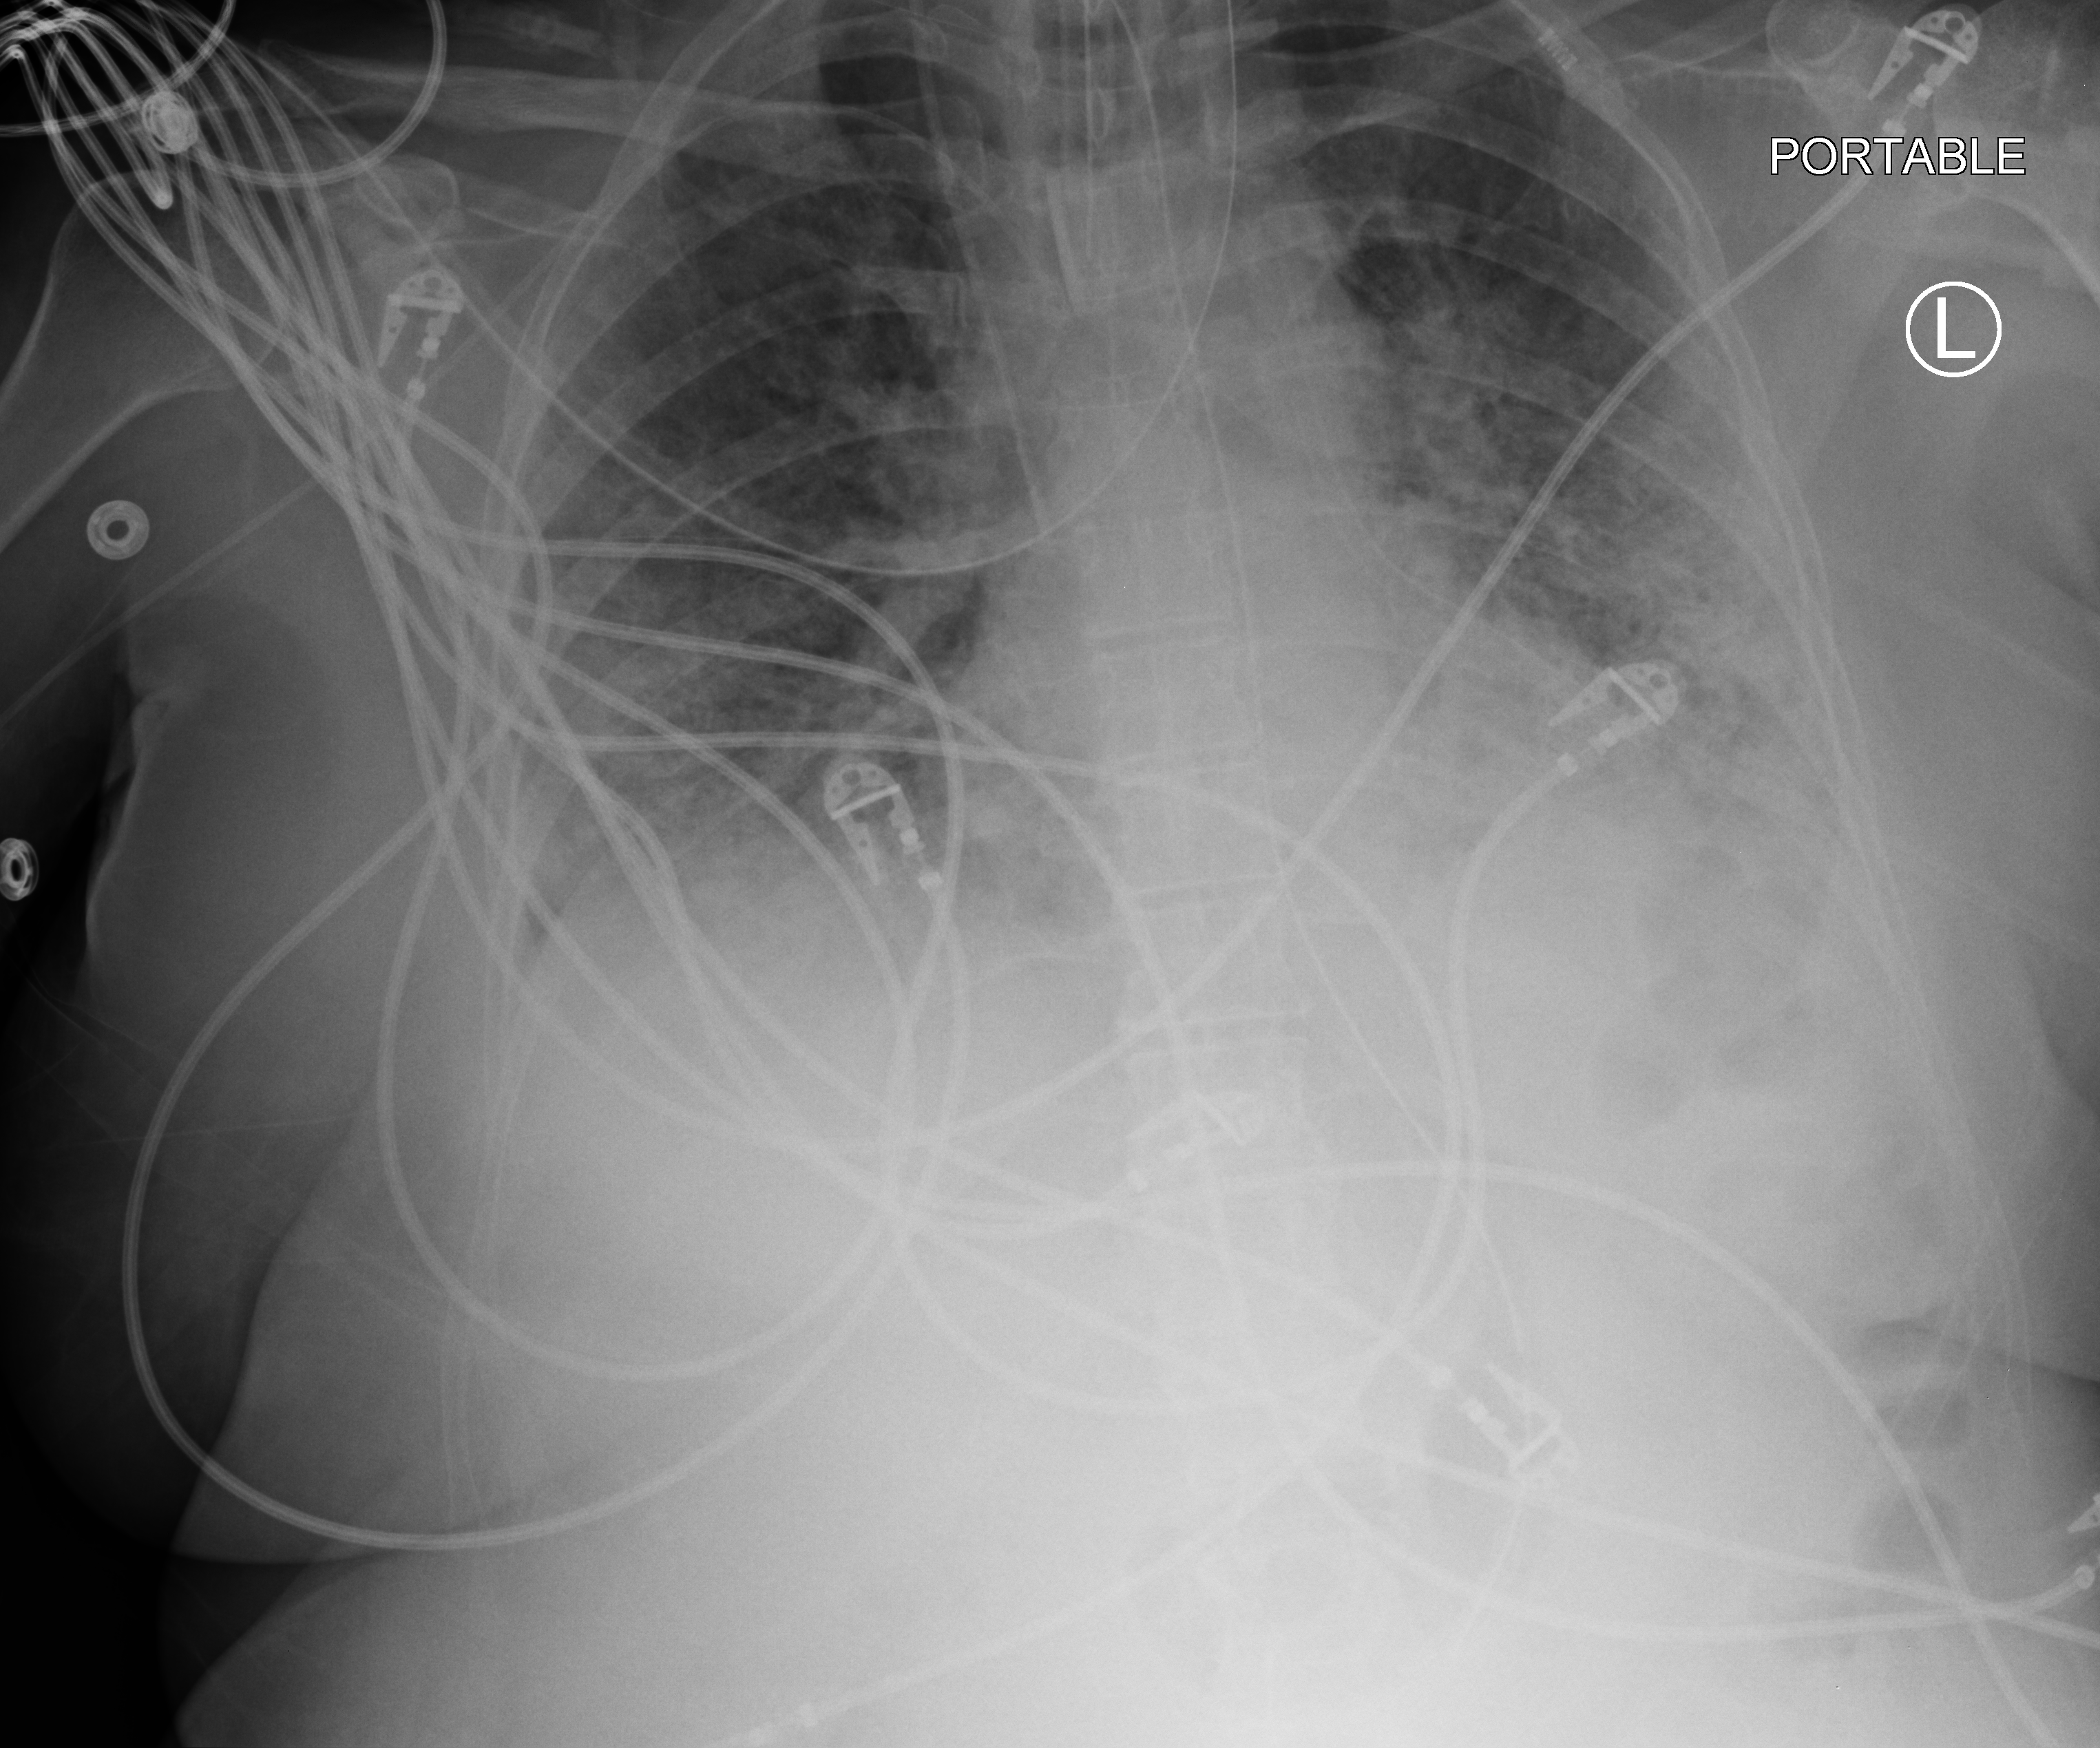
Bedside chest radiograph (computed radiography); anteroposterior (AP) projection. Patient hospitalised with COVID-19; female, aged 60–74 years.
Admission-level facts for this patient (not findings on this image; timing relative to this image not recorded): hypertension (admission record): yes.